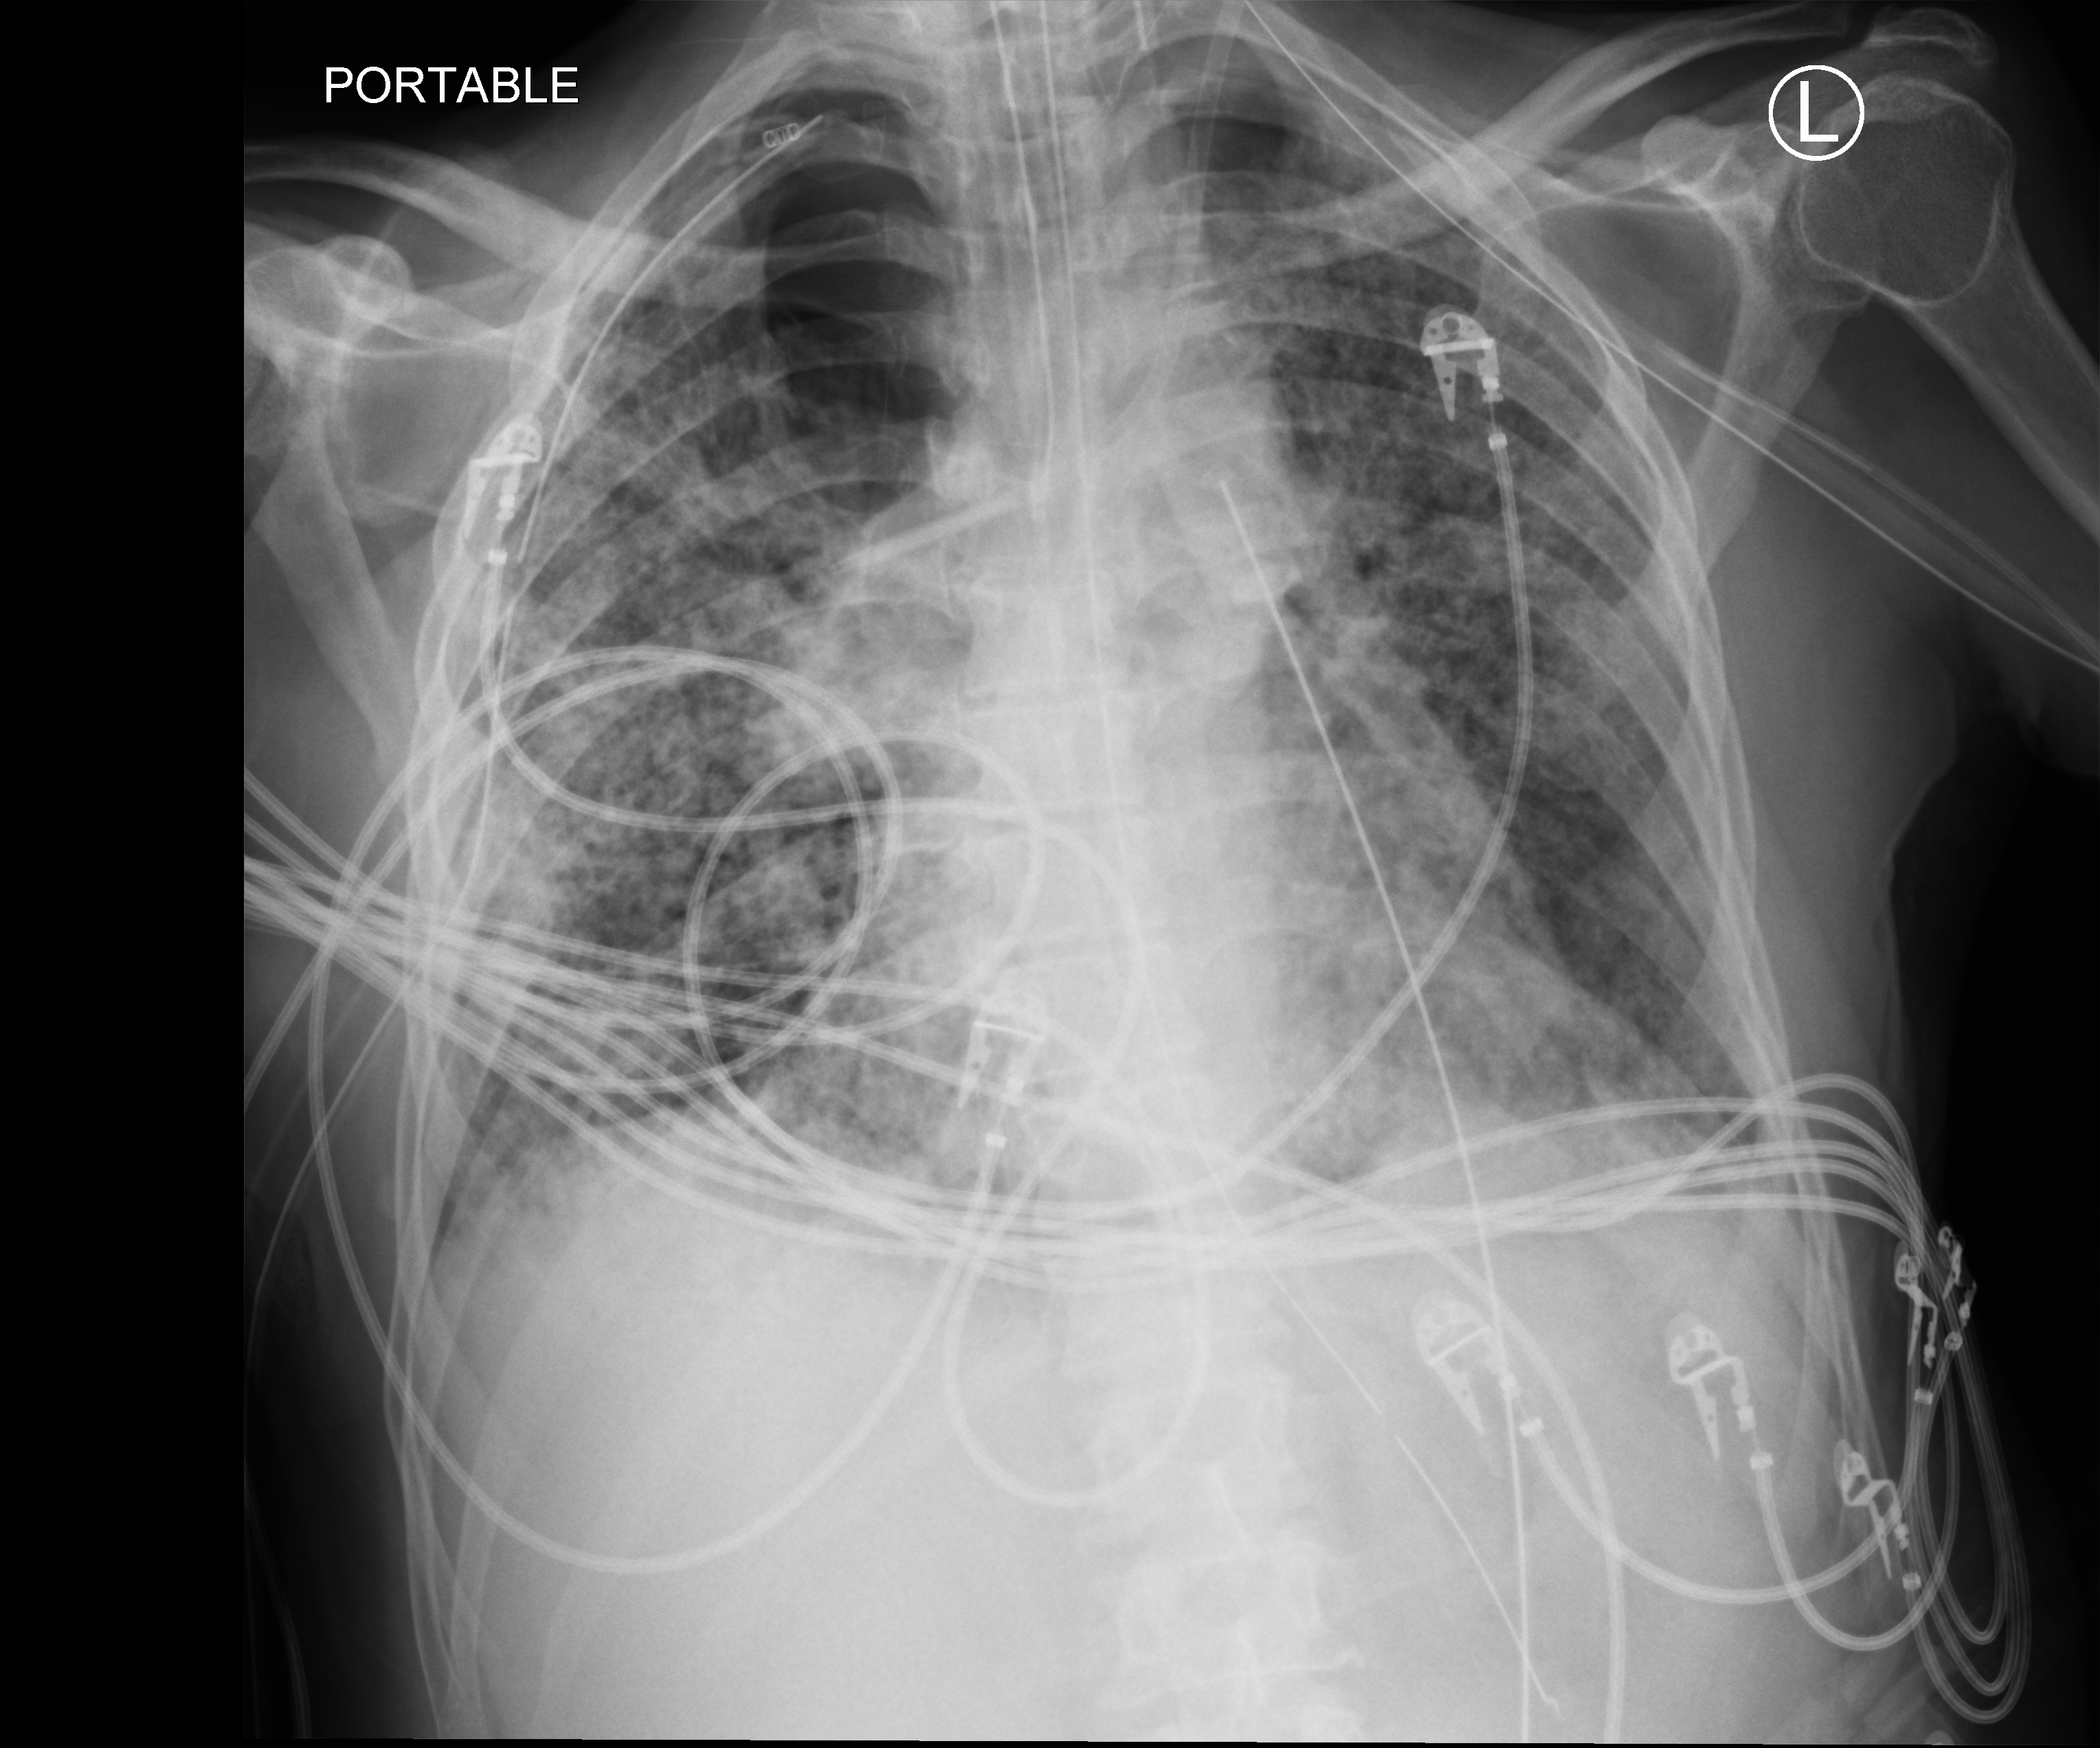
Bedside chest radiograph (computed radiography), anteroposterior (AP) projection. Patient hospitalised with COVID-19; male, aged 60–74 years.
From the hospital-stay record, not from the radiograph (when in the stay this image was taken is not recorded): length of hospital stay: 65 days; smoking status (admission record): never; mechanically ventilated during this hospital stay: yes.